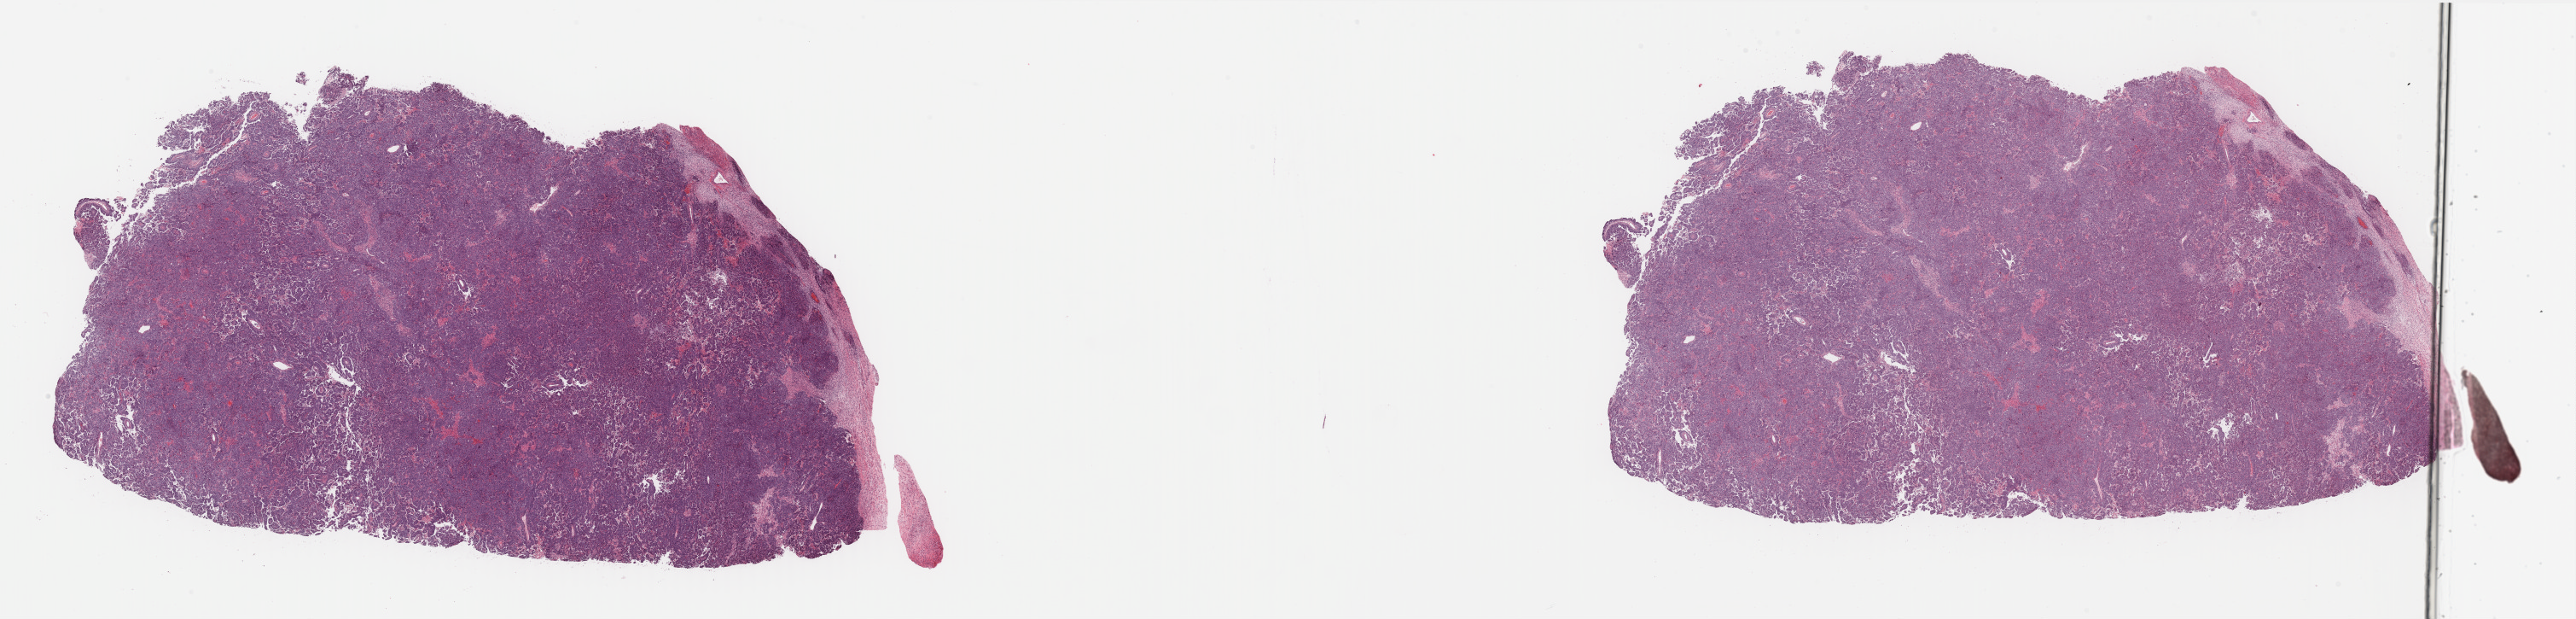
Whole-slide histology image, H&E-stained — a low-resolution overview of the entire scanned area, about 47.8 x 11.5 mm (from a 40x scan). Formalin-fixed paraffin-embedded (FFPE) diagnostic section. Testis, primary tumour sample. Patient: male, age at initial diagnosis 23 years.
* diagnosis: Embryonal carcinoma, NOS